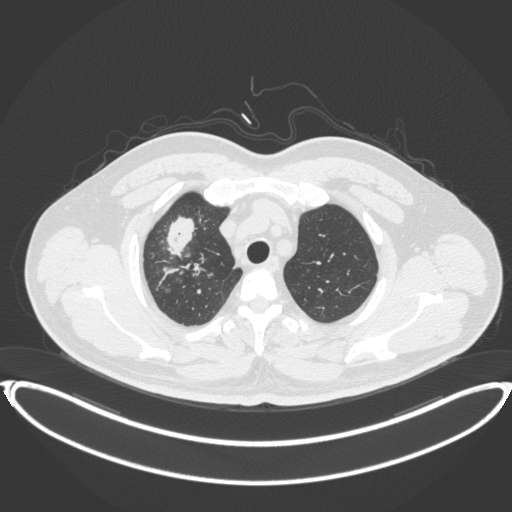
Chest CT, one axial slice. Reconstruction kernel B31f. 120 kVp. Lung window (W 1500 / L -600 HU). 512 × 512 image matrix. Male patient, age 53 years. From the clinical record (not read from this slice): clinical TNM (as recorded): T2a N0 M0.
Structures marked on this image (rectangle marked by the reading radiologist):
- lung tumour (recorded histology: adenocarcinoma): bounding box (x1, y1, x2, y2) in pixels: (166, 213, 198, 260)